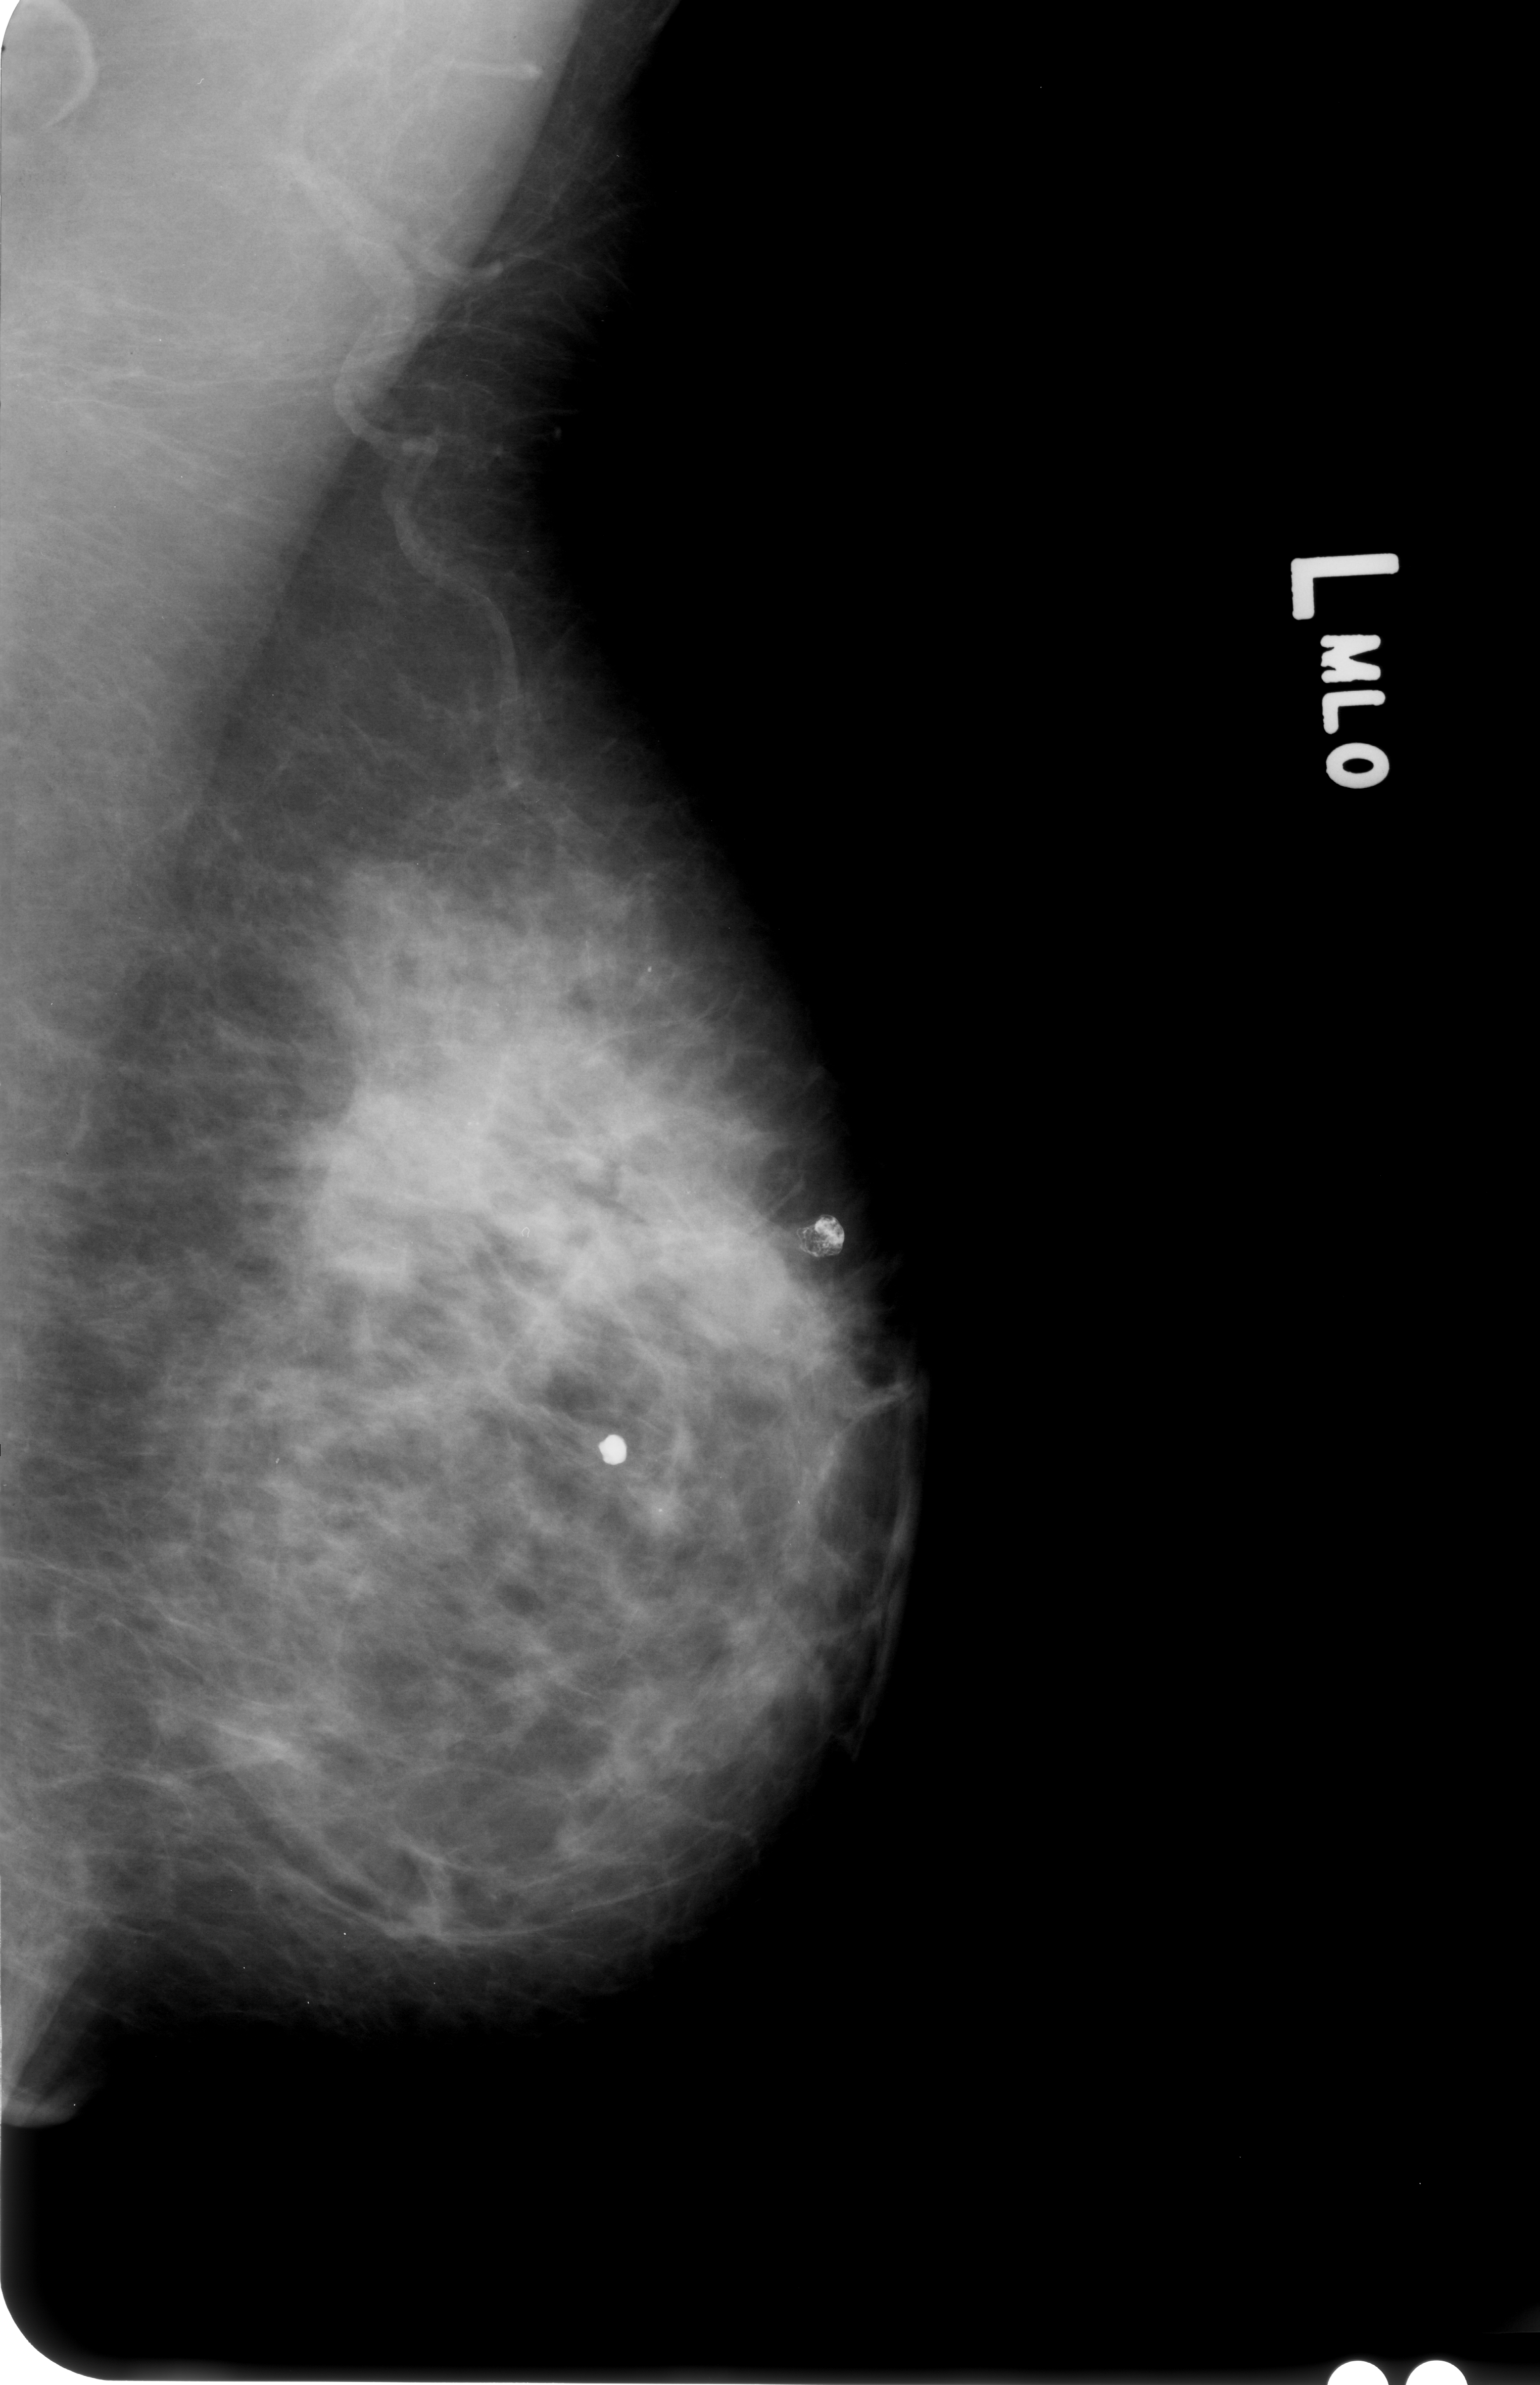
Mammogram (digitized film). Left breast. Mediolateral oblique (MLO) view. BI-RADS breast density category 3 (scale 1–4). 1540 × 2385 image matrix.
Expert-marked regions of interest on this image (one box per marked abnormality):
- calcifications, morphology punctate, distribution segmental; BI-RADS assessment category 4; pathology result (as recorded, not read from the image): malignant: bounding box (x1, y1, x2, y2) in pixels: (238, 836, 838, 1396)